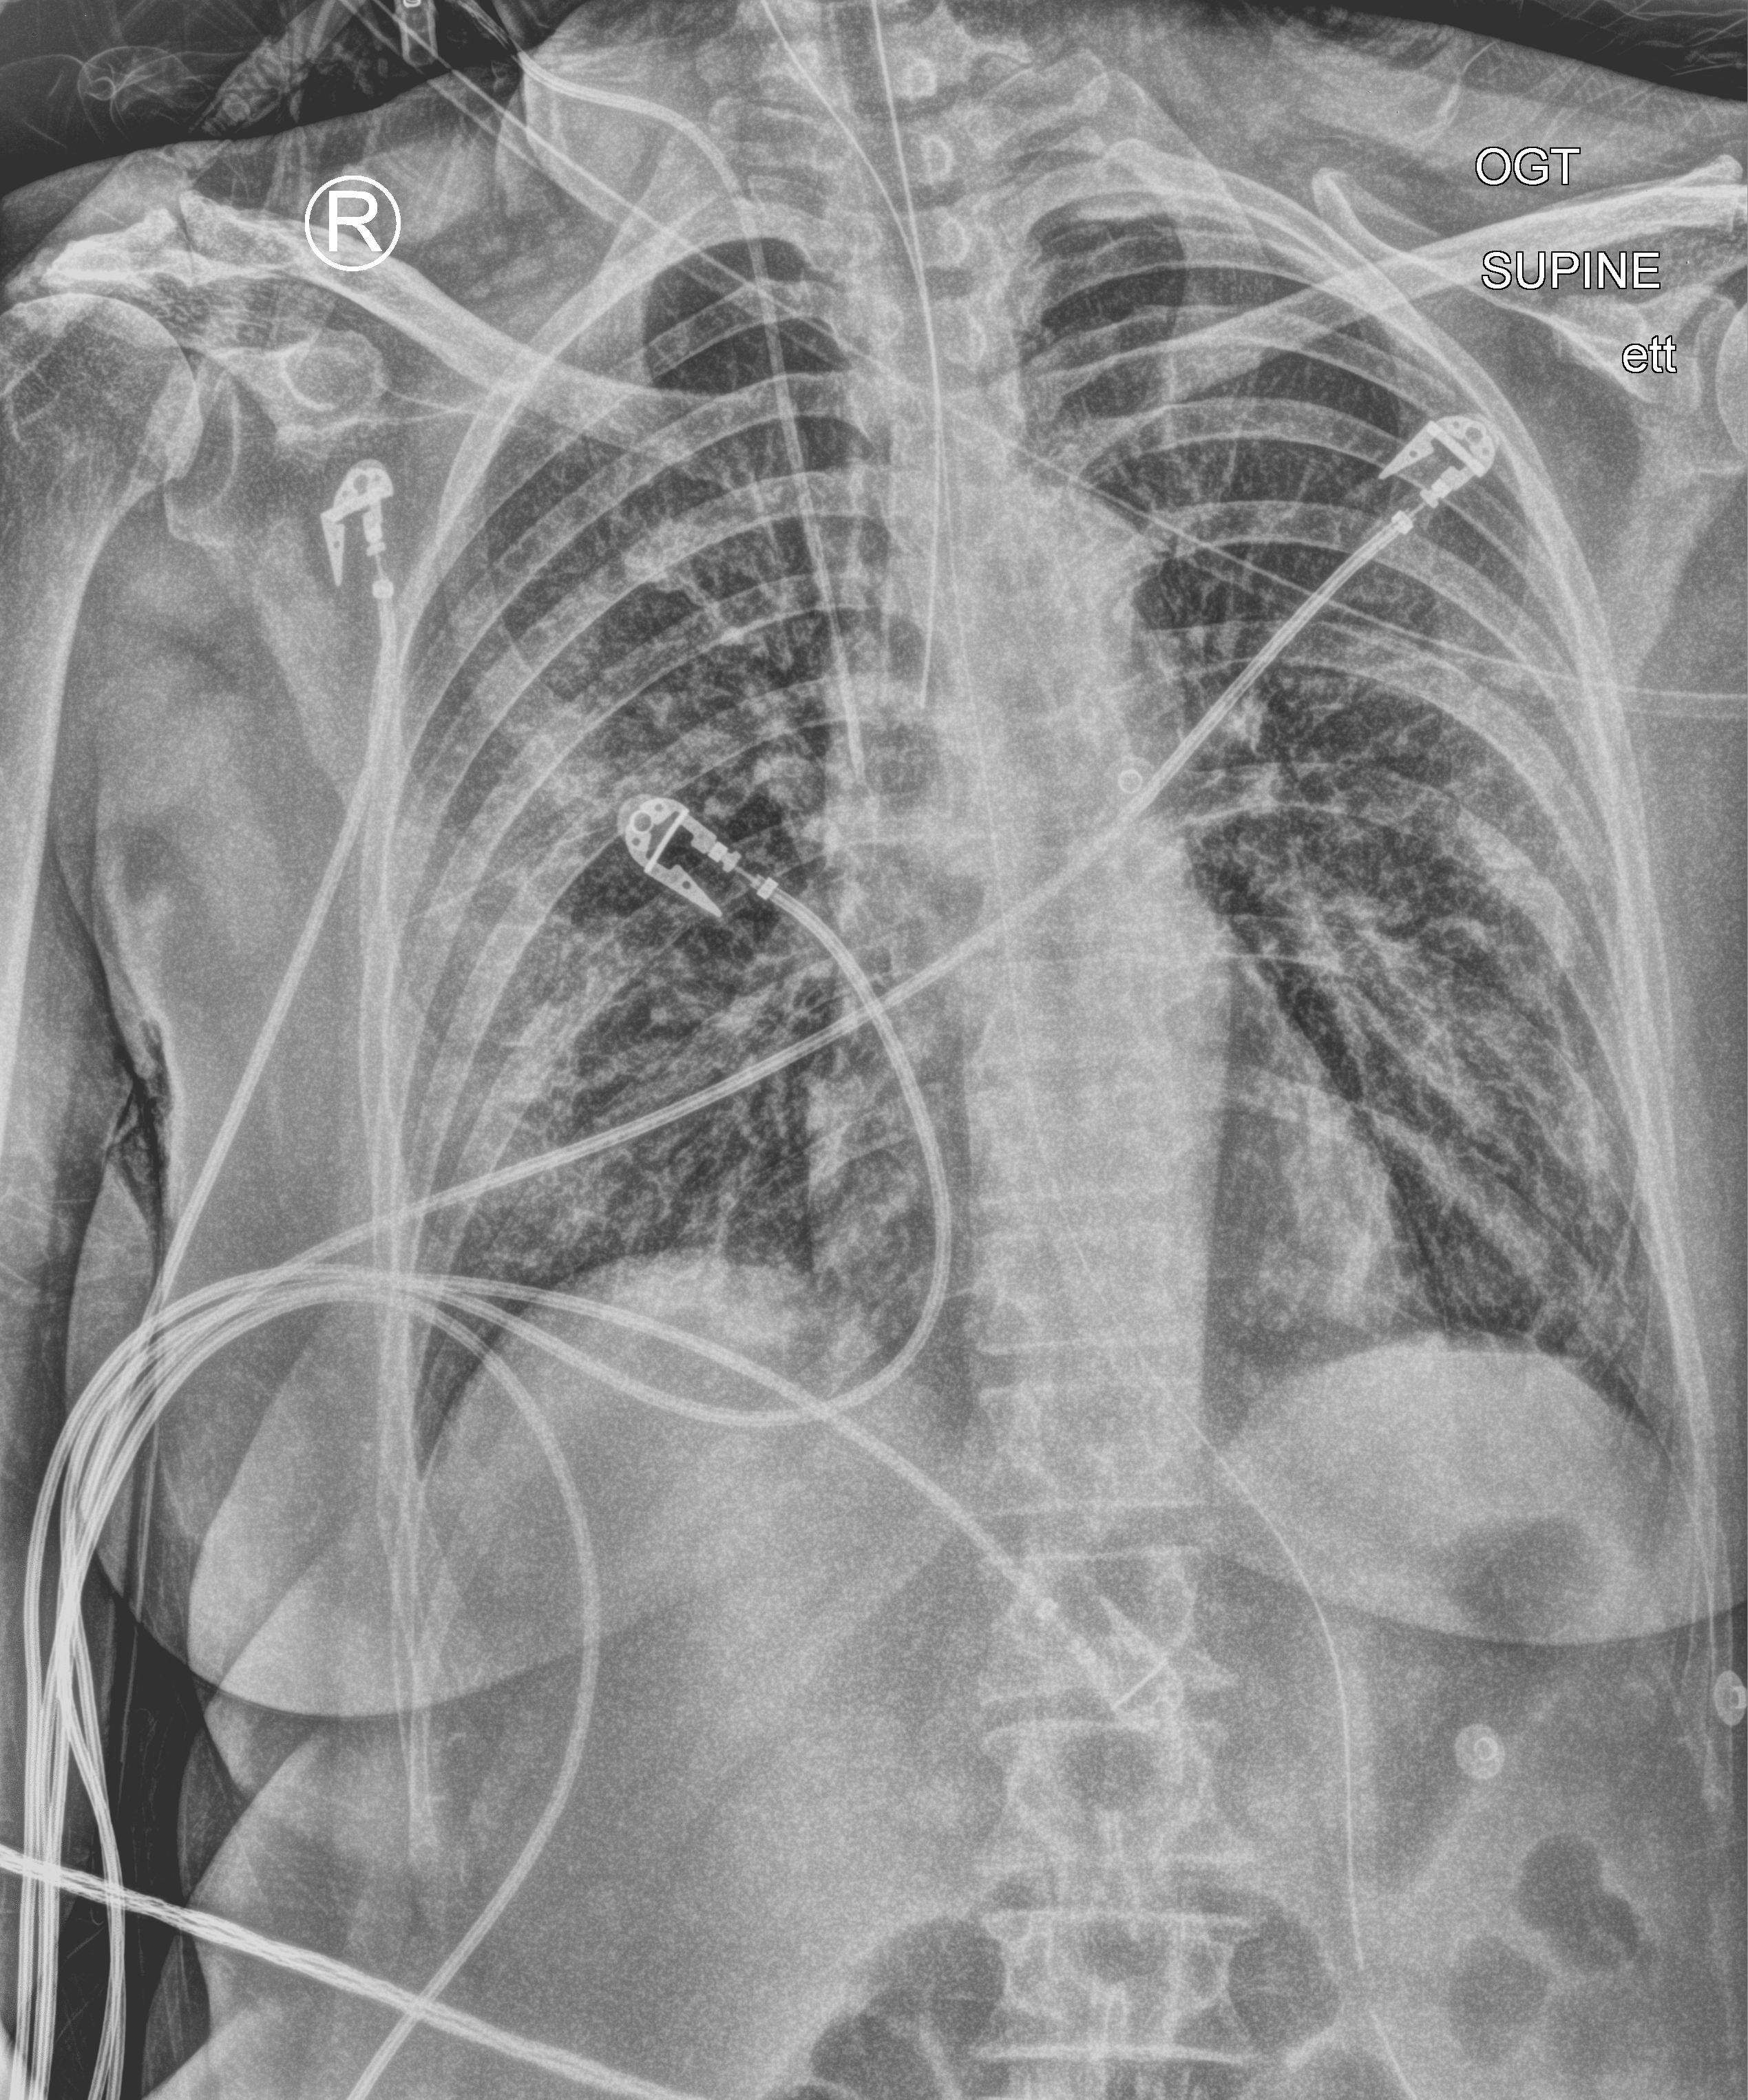
Bedside chest radiograph (computed radiography). Patient hospitalised with COVID-19; female, aged 60–74 years.
From the hospital-stay record, not from the radiograph (when in the stay this image was taken is not recorded):
- mechanically ventilated during this hospital stay: yes